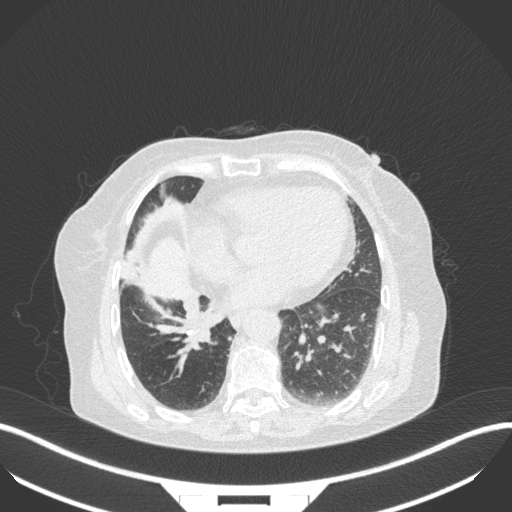
Chest CT, one axial slice. Slice 116 of 329 in the series (ordered by position). Lung window (W 1500 / L -600 HU). 1 mm slice thickness. 512 × 512 image matrix, field of view 400 × 400 mm. Patient: female, 75 years. Case-level facts recorded for this patient, not image findings: clinical TNM (as recorded): T1b N0 M1a.
Outlined on this slice (bounding box drawn by a radiologist):
- lung tumour (recorded histology: squamous cell carcinoma): box from (x=179, y=303) to (x=216, y=349) px